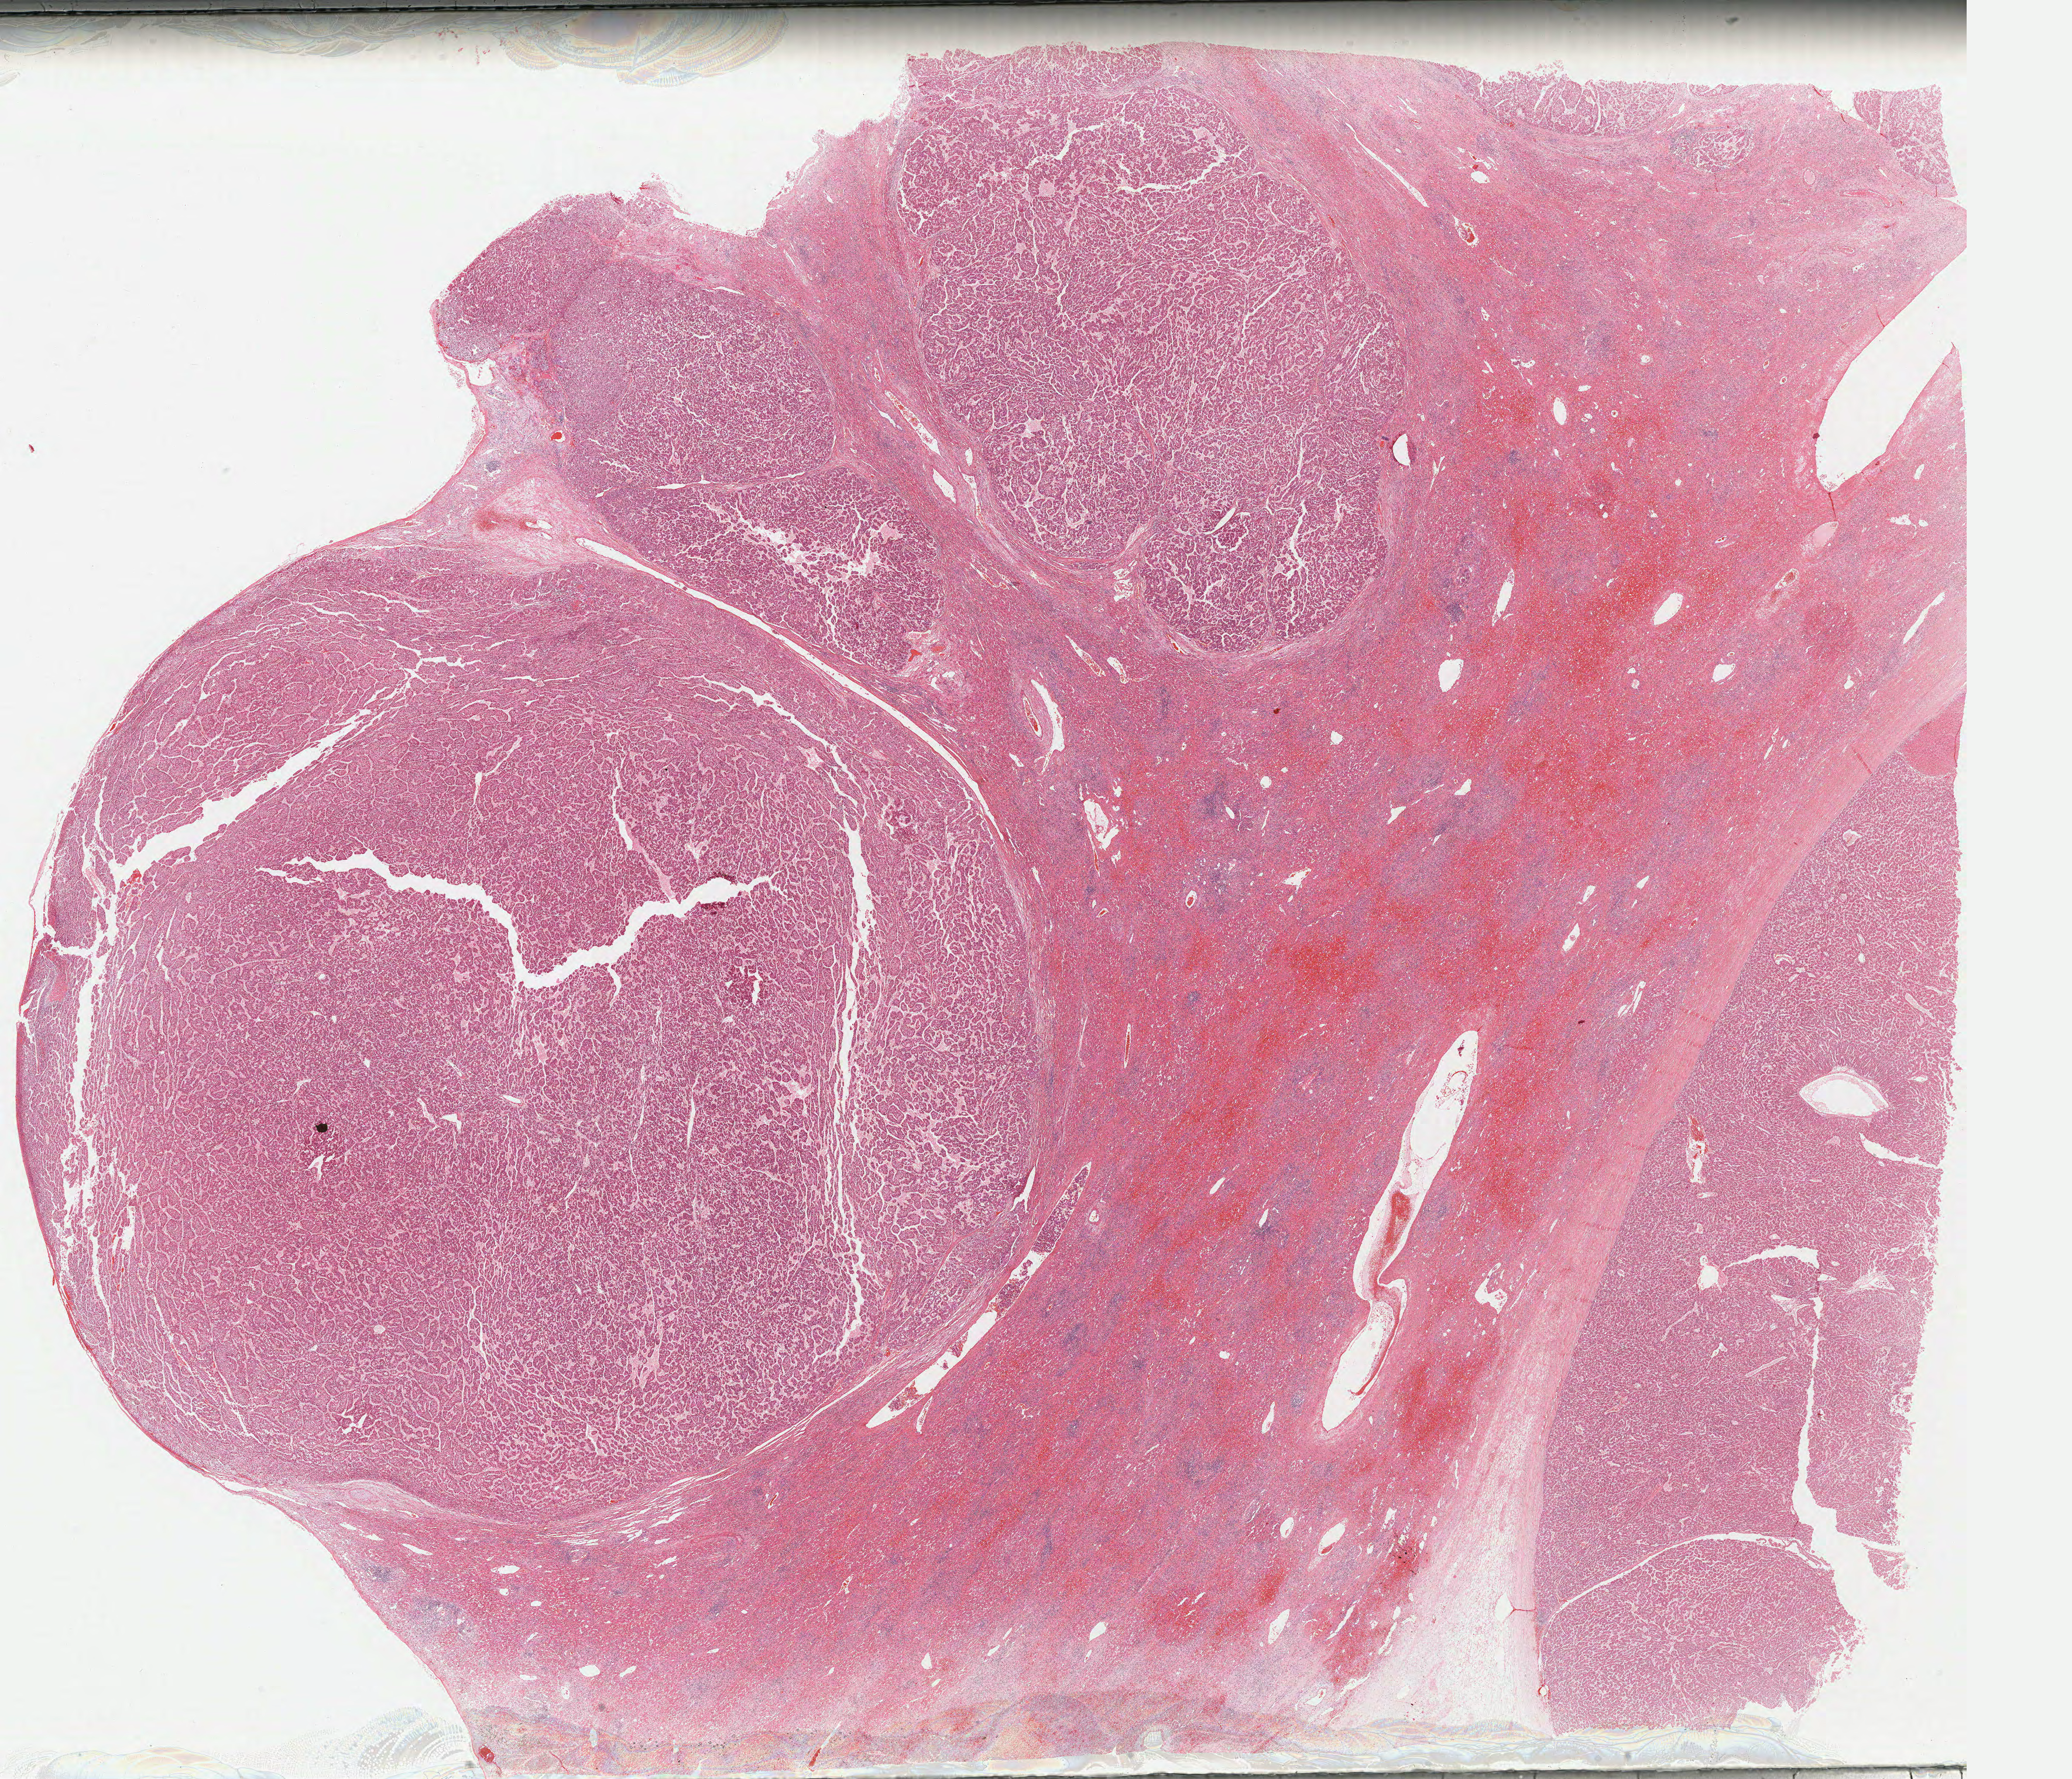
Hematoxylin and eosin (H&E) stained whole-slide image, shown as a low-resolution overview of the whole scanned area (about 28.0 x 24.0 mm). FFPE section. Primary tumour sample from the liver. Male patient; age at initial diagnosis 56 years. Histologic grade: G2 (moderately differentiated).
* AJCC pathologic stage: IIIA (6th edition)
* diagnosis: Hepatocellular carcinoma, NOS